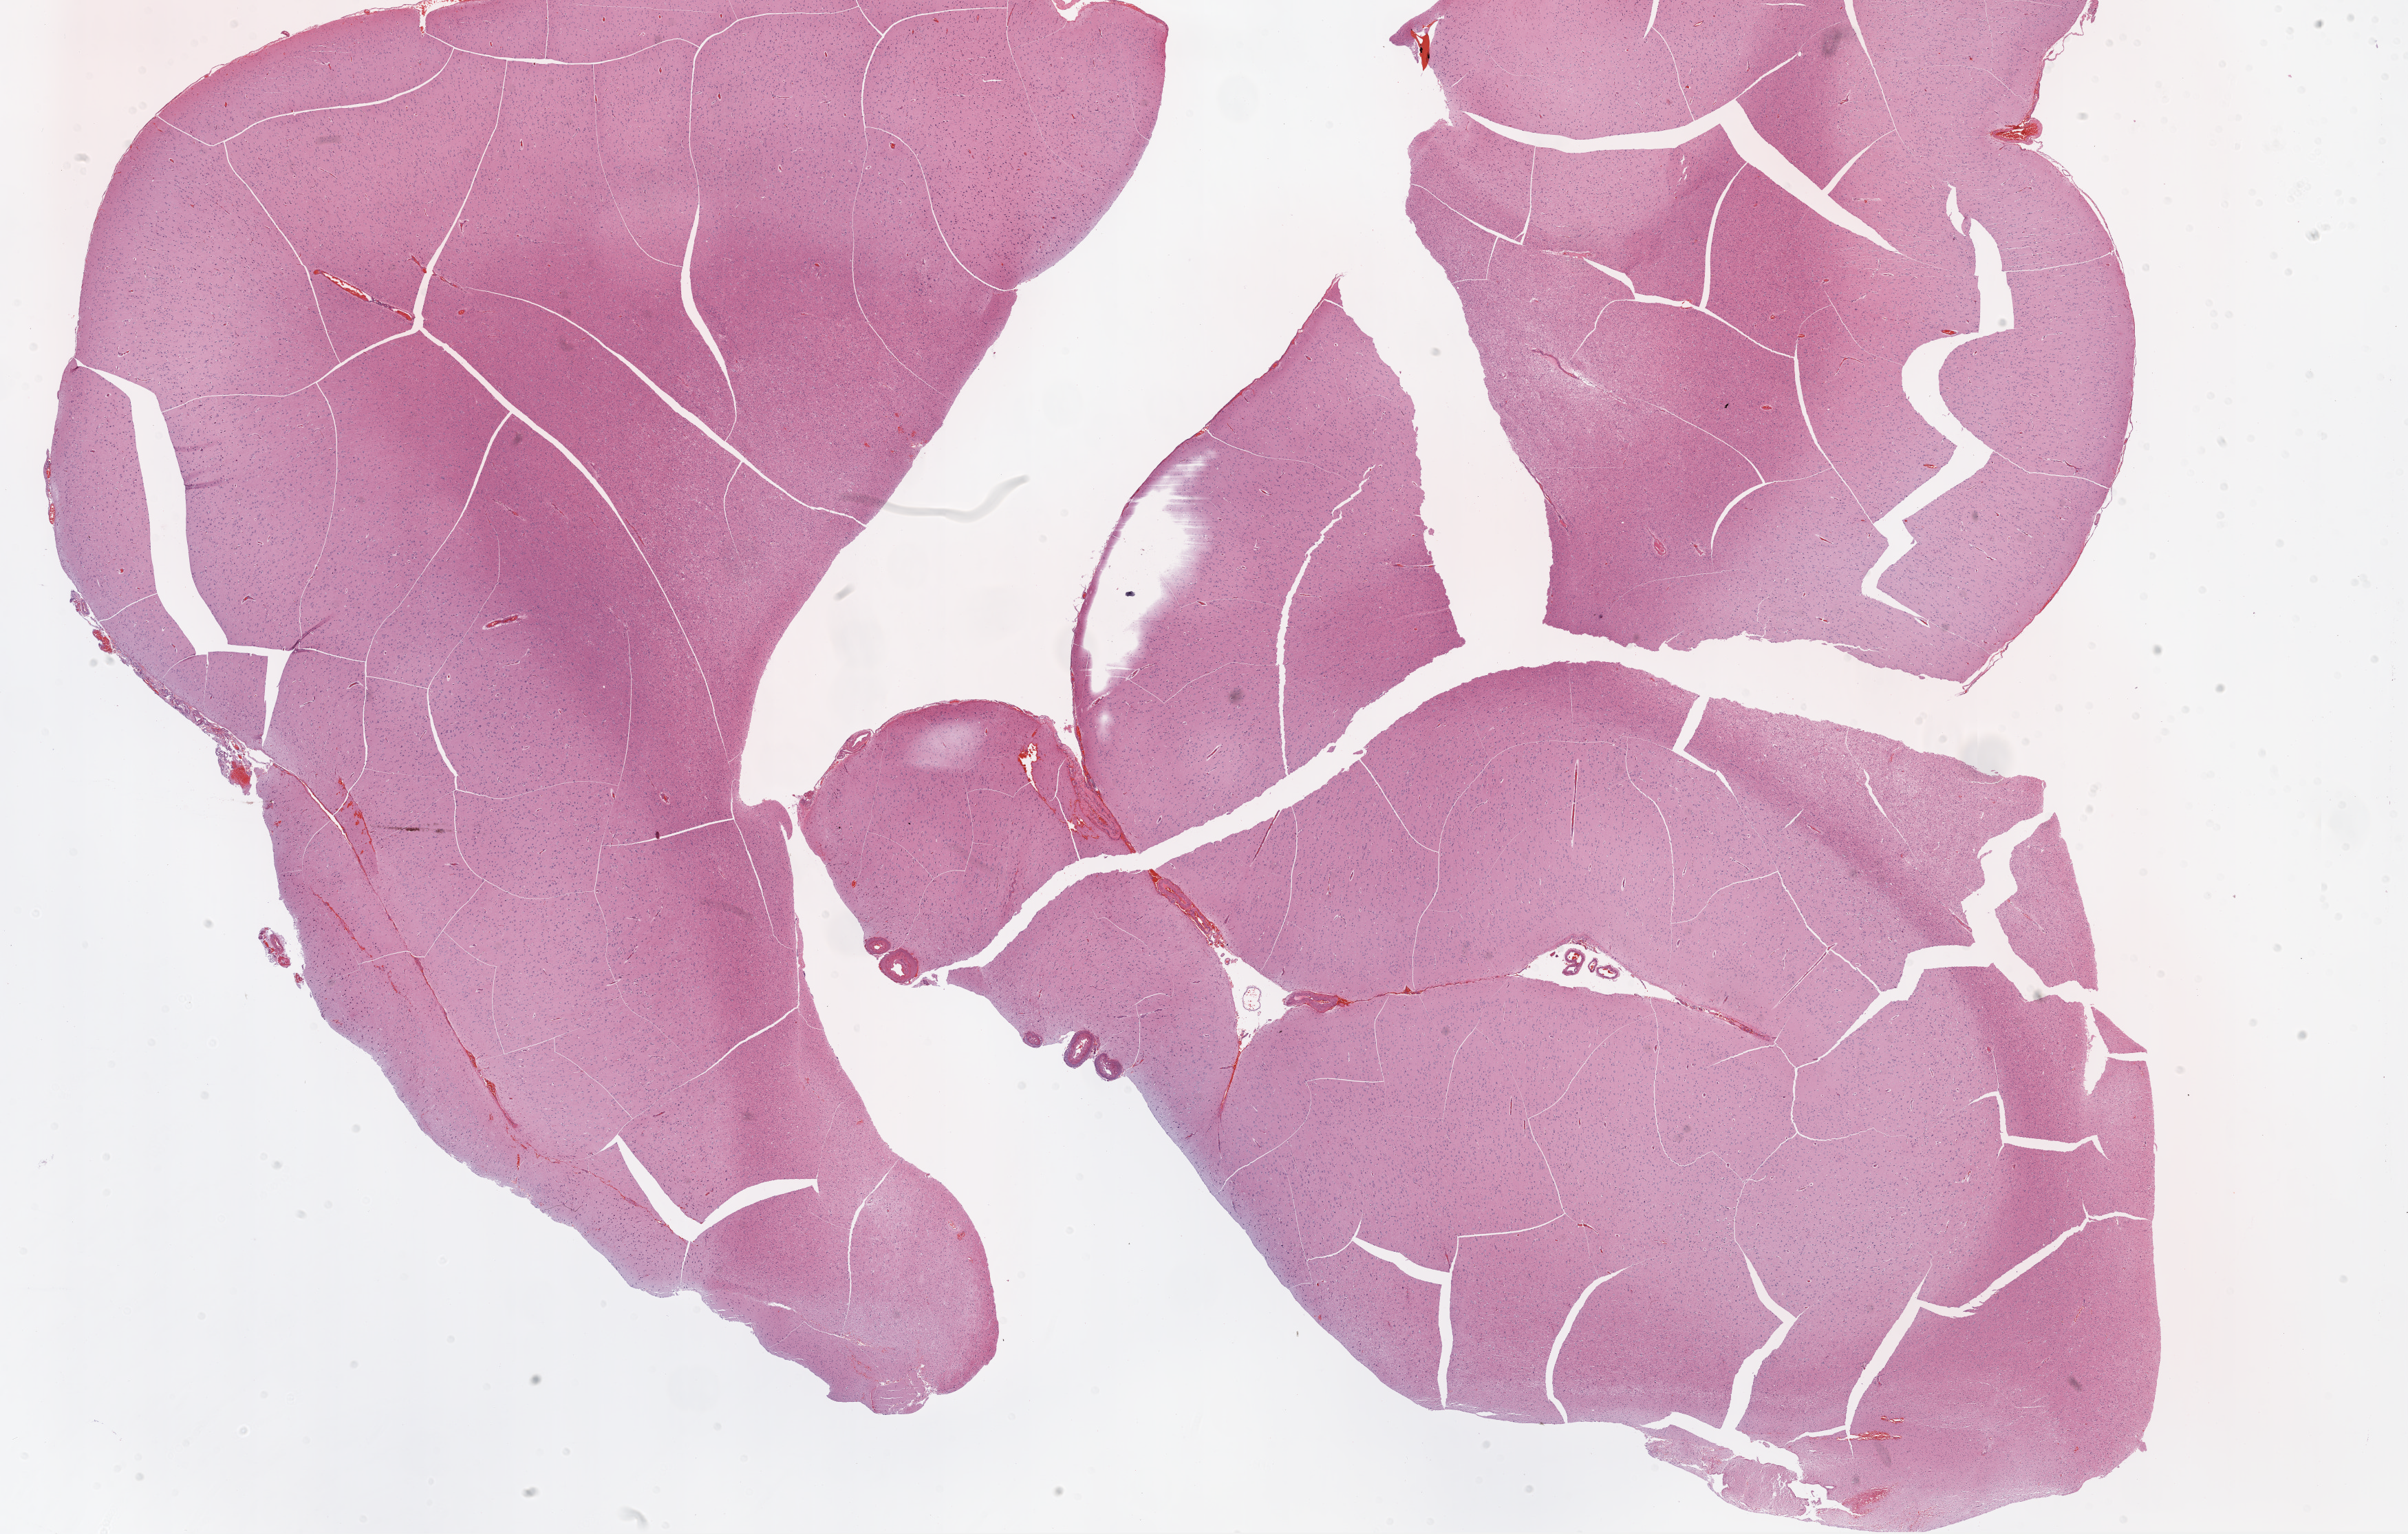
Digitized H&E tissue section (whole slide), a low-resolution overview of the entire scanned area, about 28.1 x 17.9 mm (slide scanned at 20x); formalin-fixed paraffin-embedded (FFPE) diagnostic section; brain, primary tumour sample. Male, age 71 years at initial diagnosis.
• pathologic diagnosis: Glioblastoma